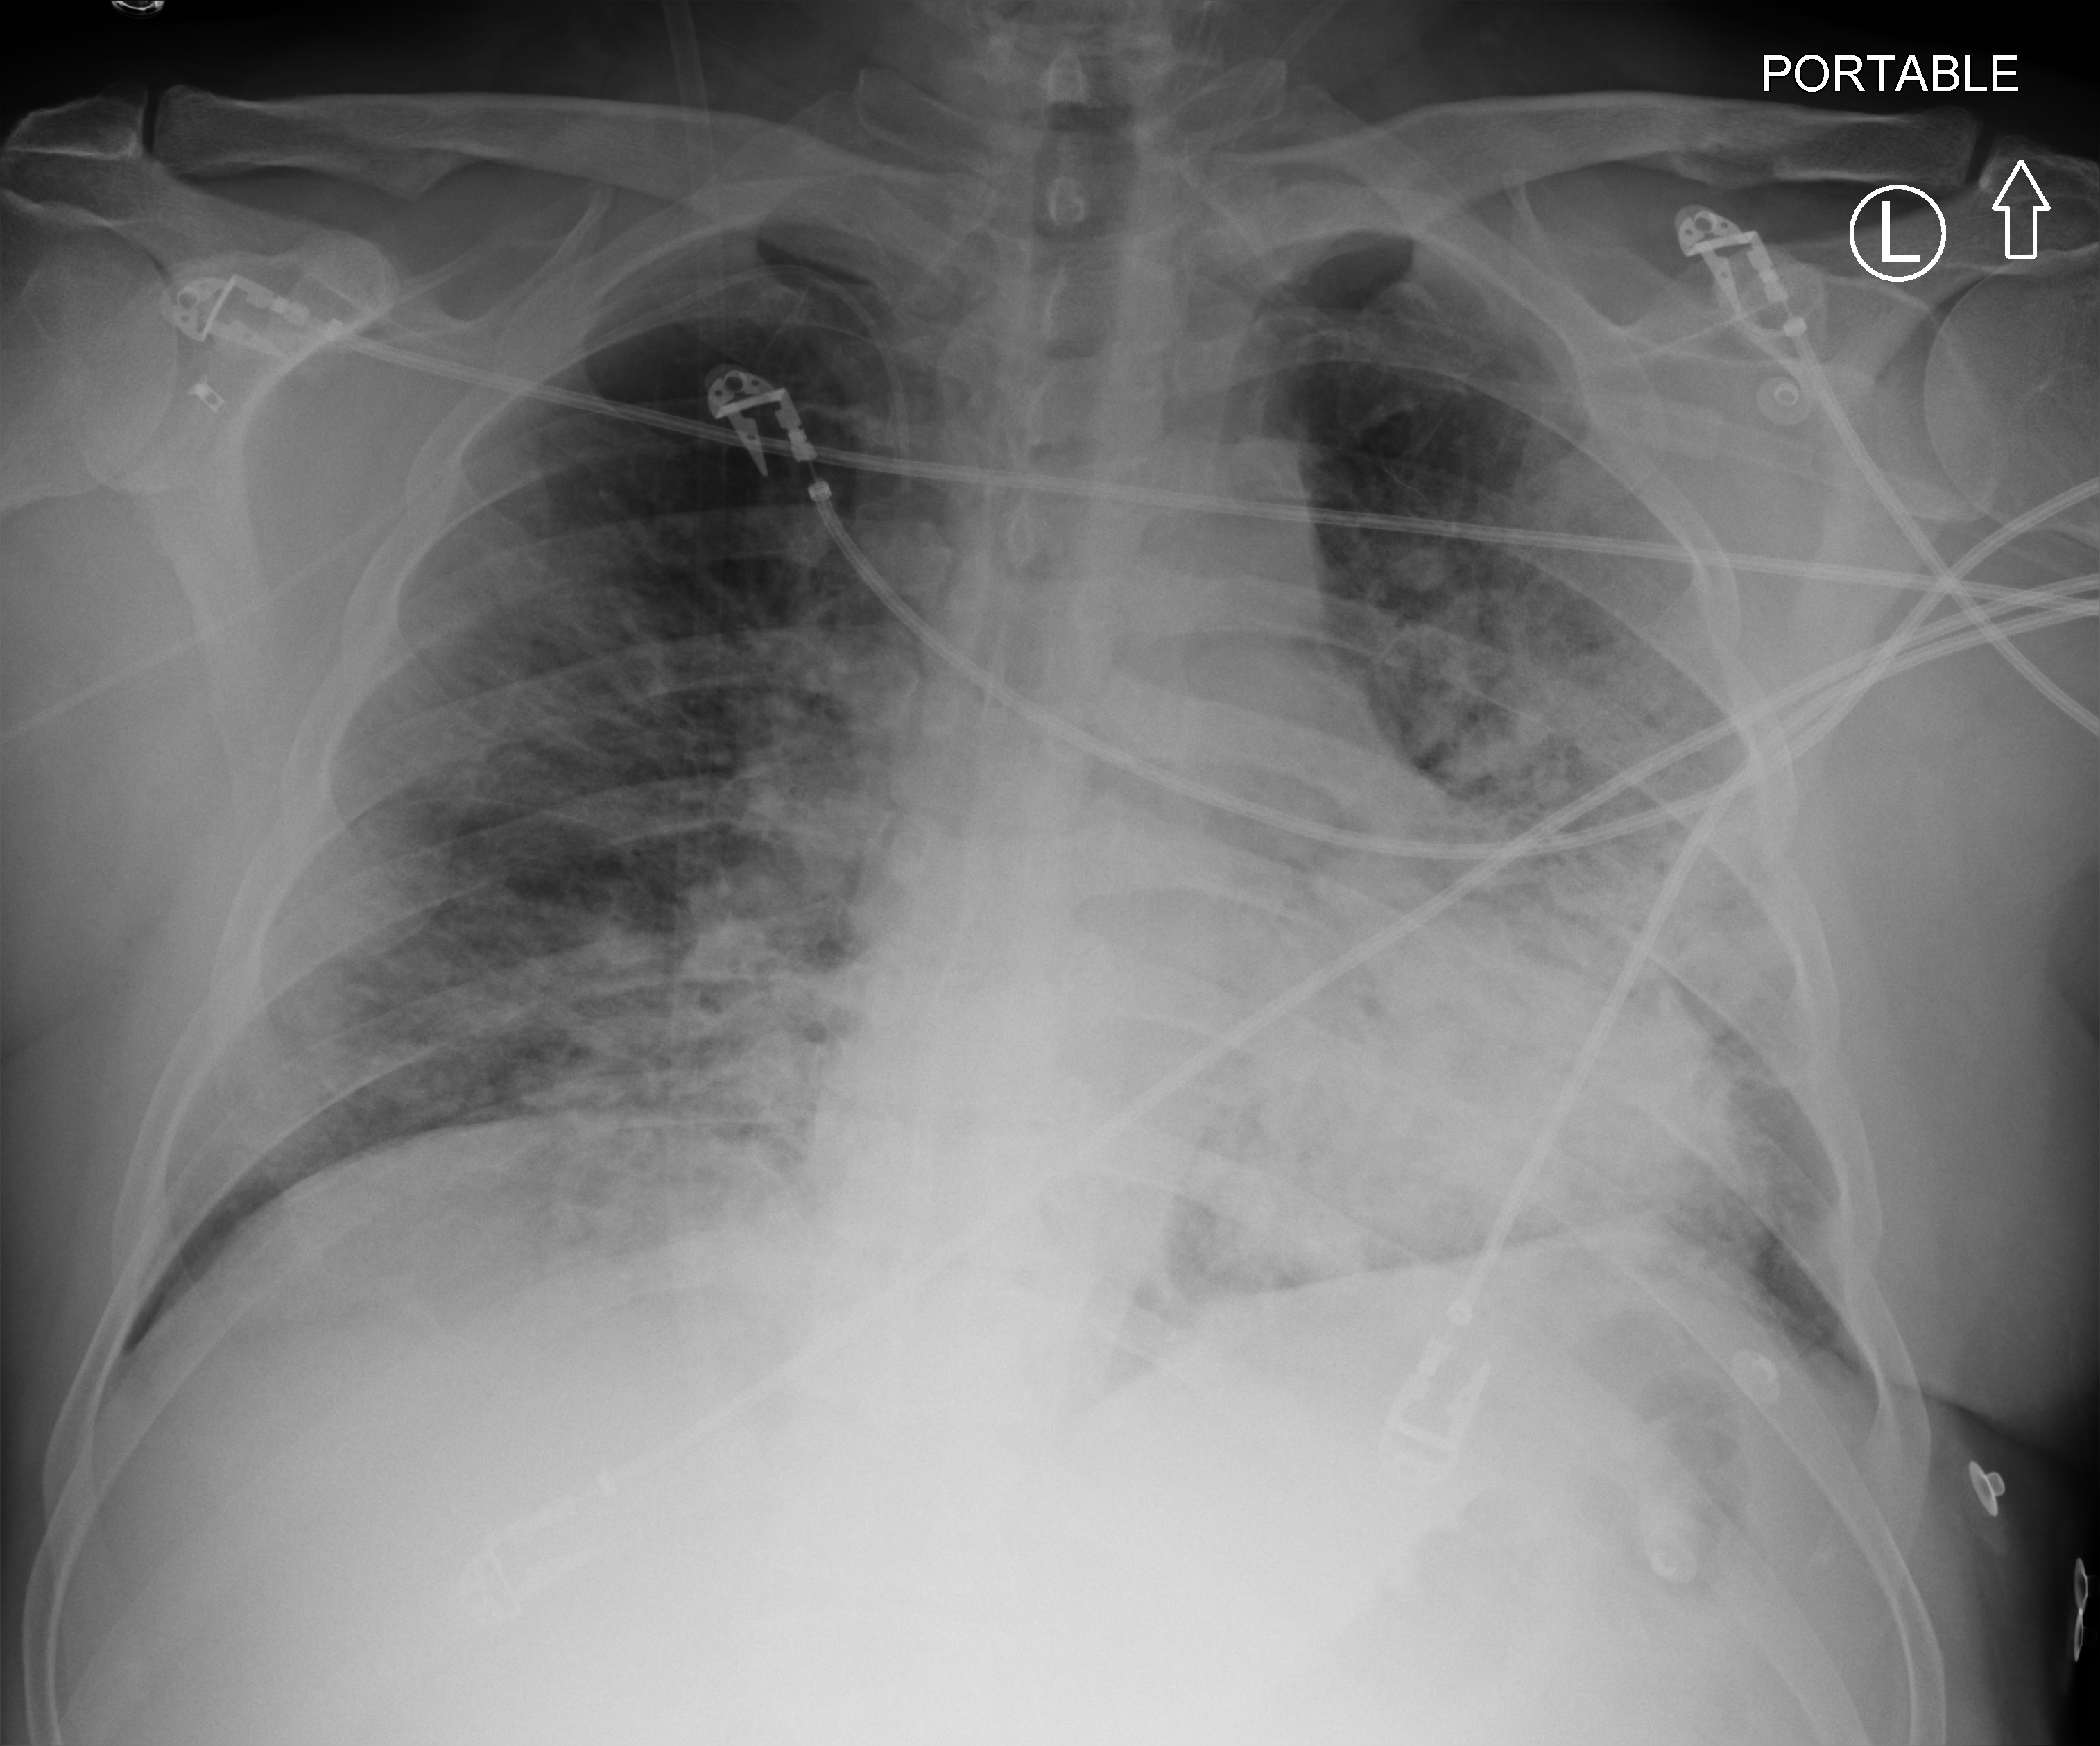
Chest X-ray (portable), anteroposterior (AP) projection. Male patient hospitalised with COVID-19, age 18–59 years.
From the hospital-stay record, not from the radiograph (when in the stay this image was taken is not recorded):
- length of hospital stay: 52 days
- smoking status (admission record): former